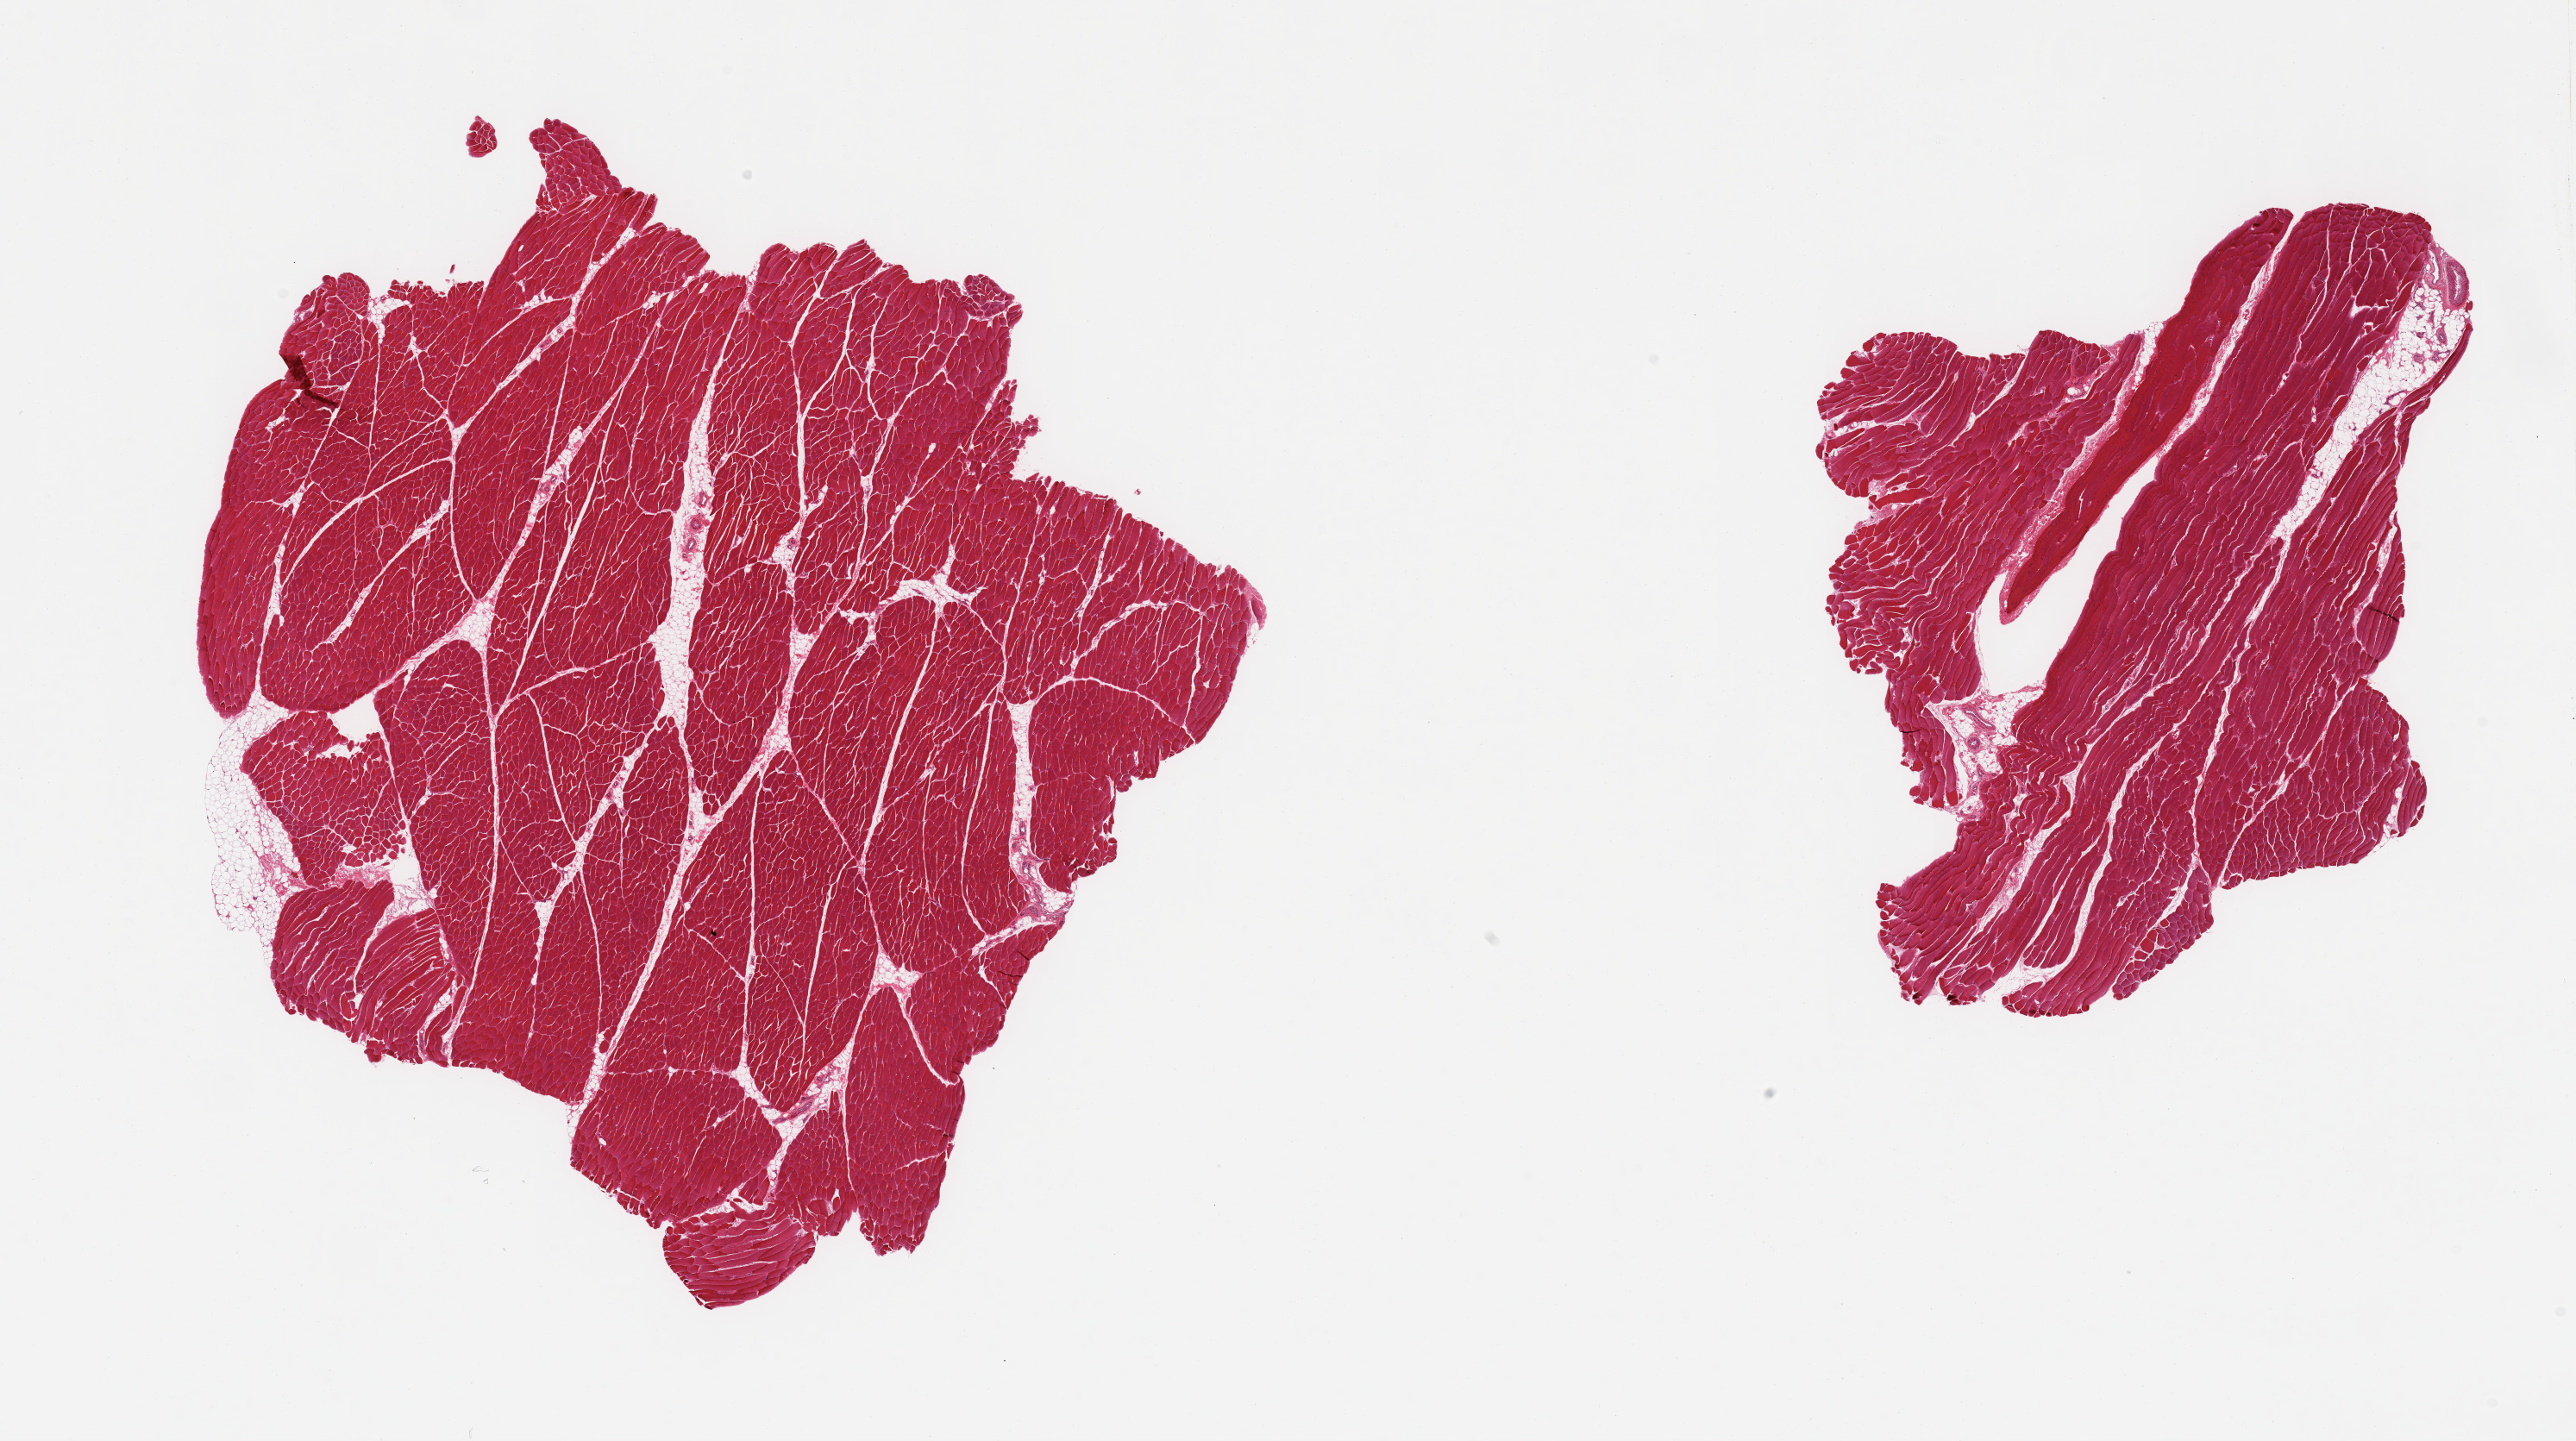
Digitized haematoxylin and eosin-stained section — low-resolution overview of the scanned area, about 23.6 x 13.2 mm. PAXgene-fixed paraffin-embedded (PFPE) section. Target tissue: skeletal muscle. Tissue donor sample. Donor: male.
Review note (as recorded): 2 pieces; ~5% internal fat and small focus of external fat.